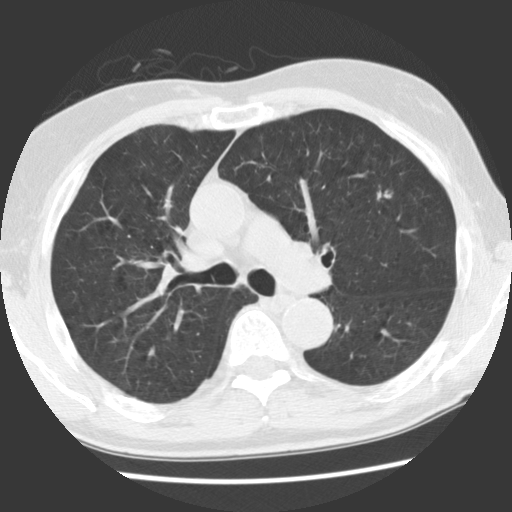
Axial slice from a low-dose chest CT screening exam; baseline annual screen; lung window (W 1500 / L -600 HU); 2.5 mm slice thickness; slice 83 of 131 in the series. Male, age 70 years at enrolment.
• Expert reader's lesion annotation, box from (x=353, y=179) to (x=403, y=223) px.
• The screening reader recorded 2 non-calcified nodules or masses ≥4 mm on this exam (left upper lobe, right lower lobe); which of them this box marks is not recorded.